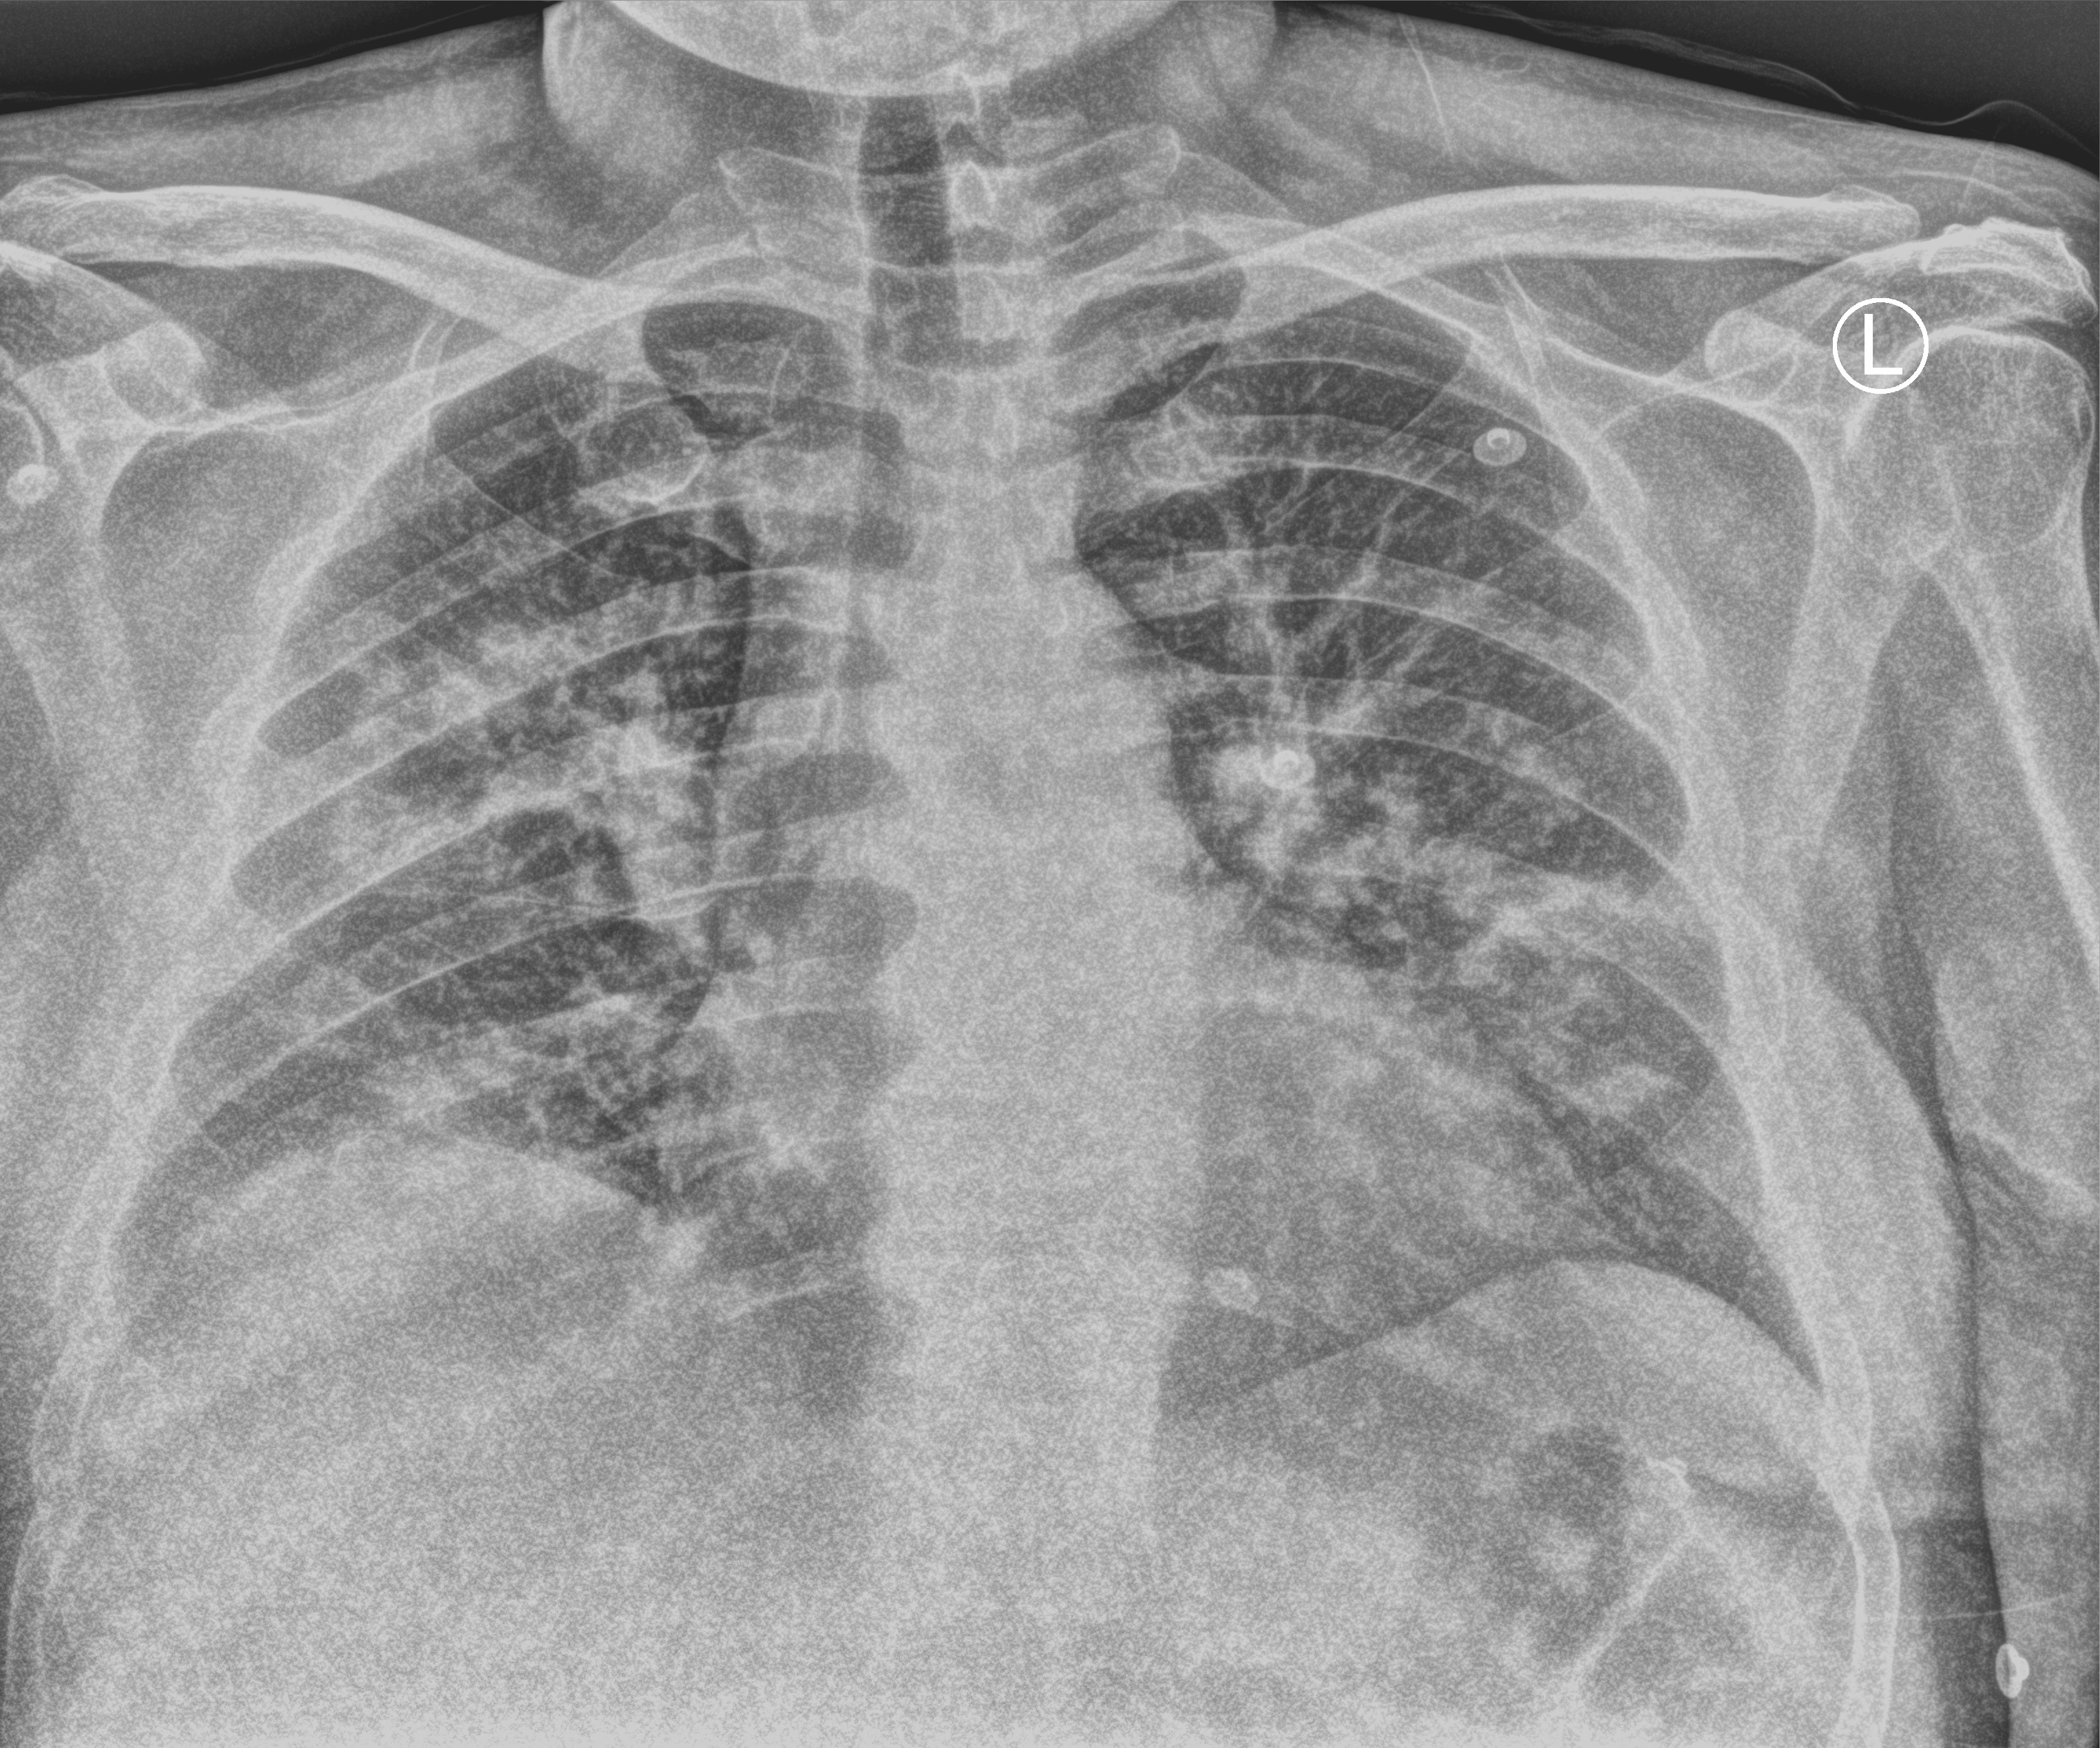
Bedside chest radiograph (computed radiography). Patient hospitalised with COVID-19; male, aged 18–59 years.
From the hospital-stay record, not from the radiograph (when in the stay this image was taken is not recorded): COPD (admission record): no; diabetes (admission record): yes; other chronic lung disease (admission record): no.